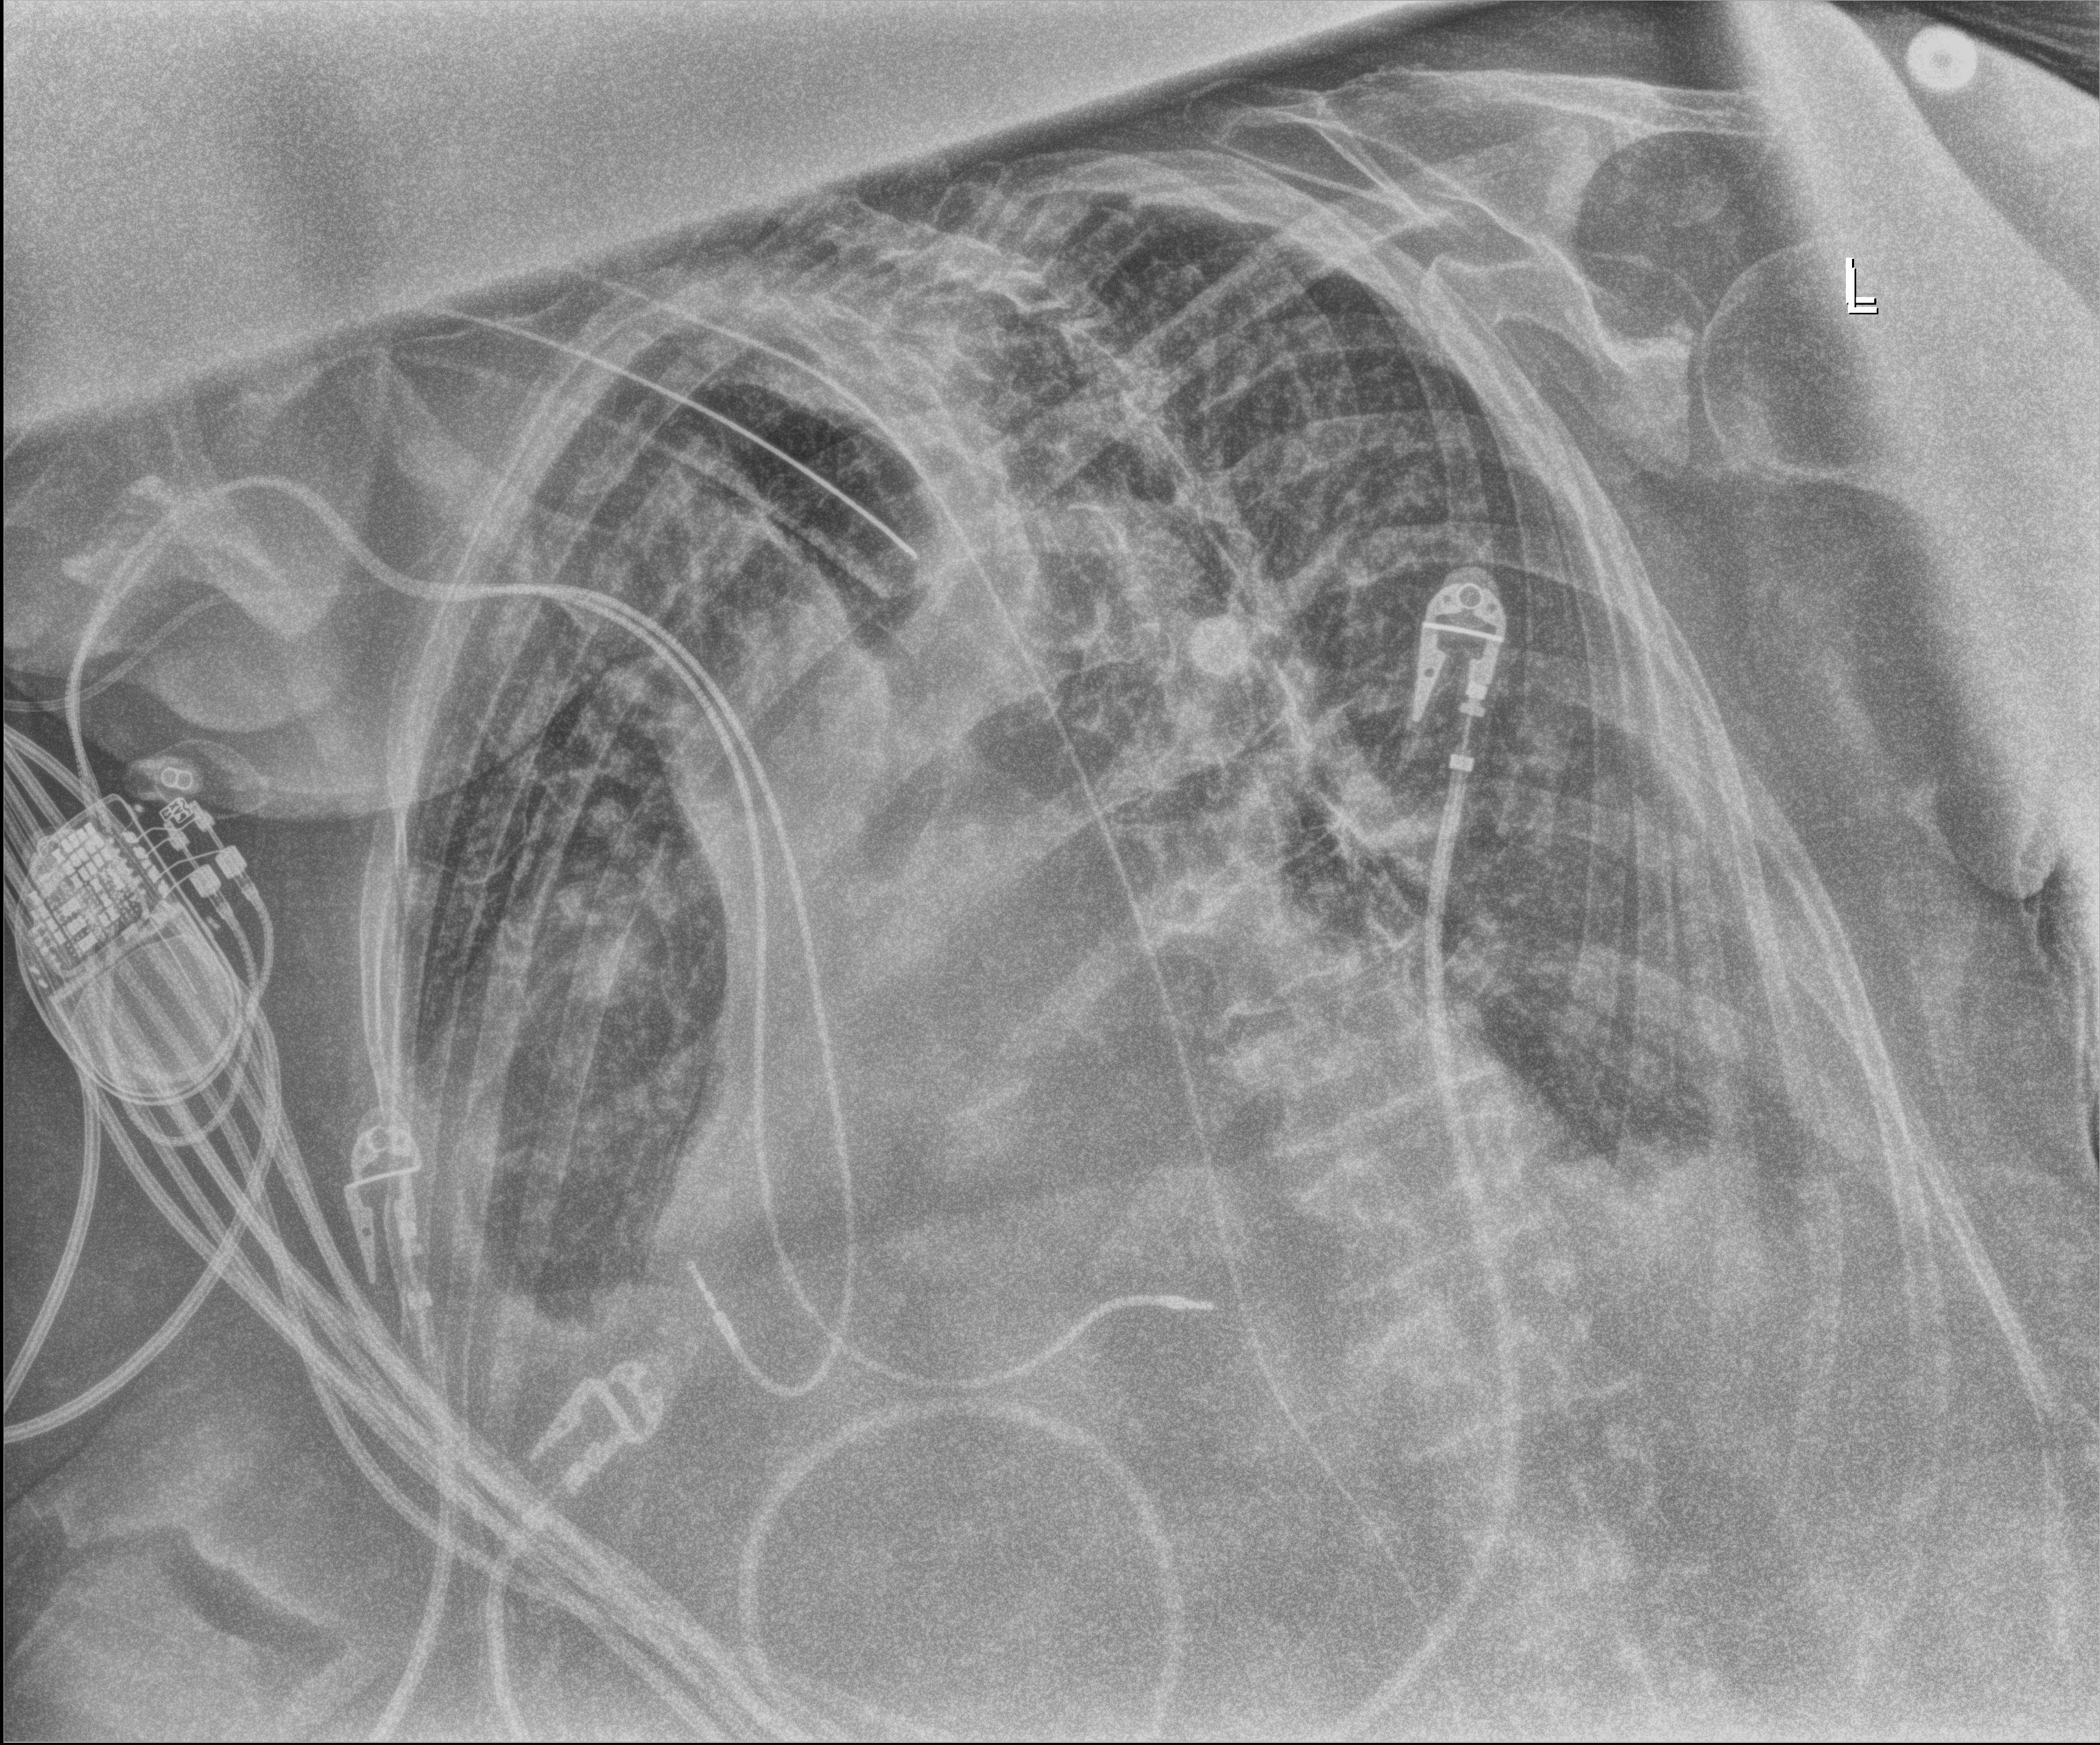
Bedside chest radiograph (digital radiography); anteroposterior (AP) projection. Female patient hospitalised with COVID-19, age 75–90 years.
Hospital-stay facts (about this admission, not read from this image; timing relative to this image not recorded): mechanically ventilated during this hospital stay: yes; COPD (admission record): yes.